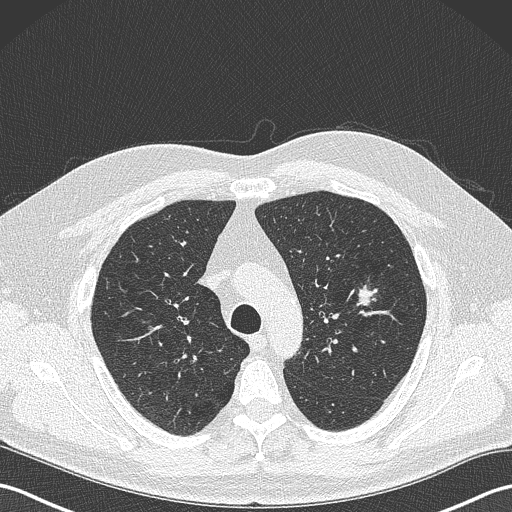
Low-dose screening chest CT, axial slice, first (baseline) screen, lung window (W 1500 / L -600 HU), 1 mm slice thickness, lung (sharp) reconstruction kernel (B50f), 120 kVp, 512 × 512 image matrix, field of view 350 × 350 mm. Male participant, aged 61 years at enrolment.
Expert reader's lesion annotation, box from (x=349, y=281) to (x=385, y=312) px. The screening reader recorded 2 non-calcified nodules or masses ≥4 mm on this exam (left upper lobe, lingula); which of them this box marks is not recorded. Official screen result: positive, change unspecified: nodule(s) >= 4 mm or enlarging nodule(s), mass(es), or other non-specific abnormalities suspicious for lung cancer. Later outcome: lung cancer diagnosed 160 days after this screen — adenocarcinoma, NOS, left upper lobe, poorly differentiated (G3), stage IA (AJCC 6th edition), 28 mm at pathology.